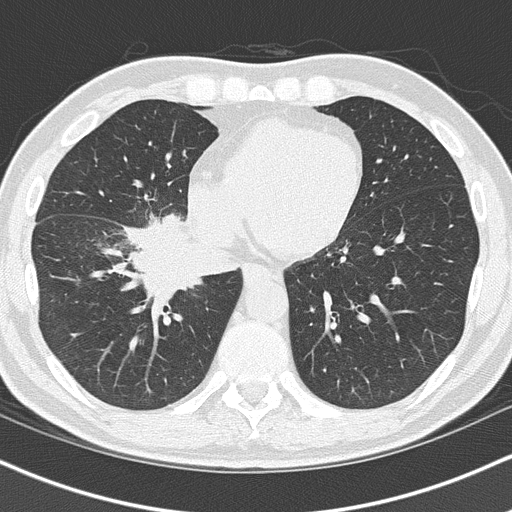
Low-dose screening chest CT, one axial slice; slice 45 of 151 in the series (ordered by position); reconstruction kernel B50f; 120 kVp; lung window (W 1500 / L -600 HU); 512 × 512 image matrix, field of view 320 × 320 mm.
Structures marked on this image (outlined manually by an expert reader):
- lesion 1 (tumor, hilum of right lung): bounding box (x1, y1, x2, y2) in pixels: (126, 215, 198, 298)